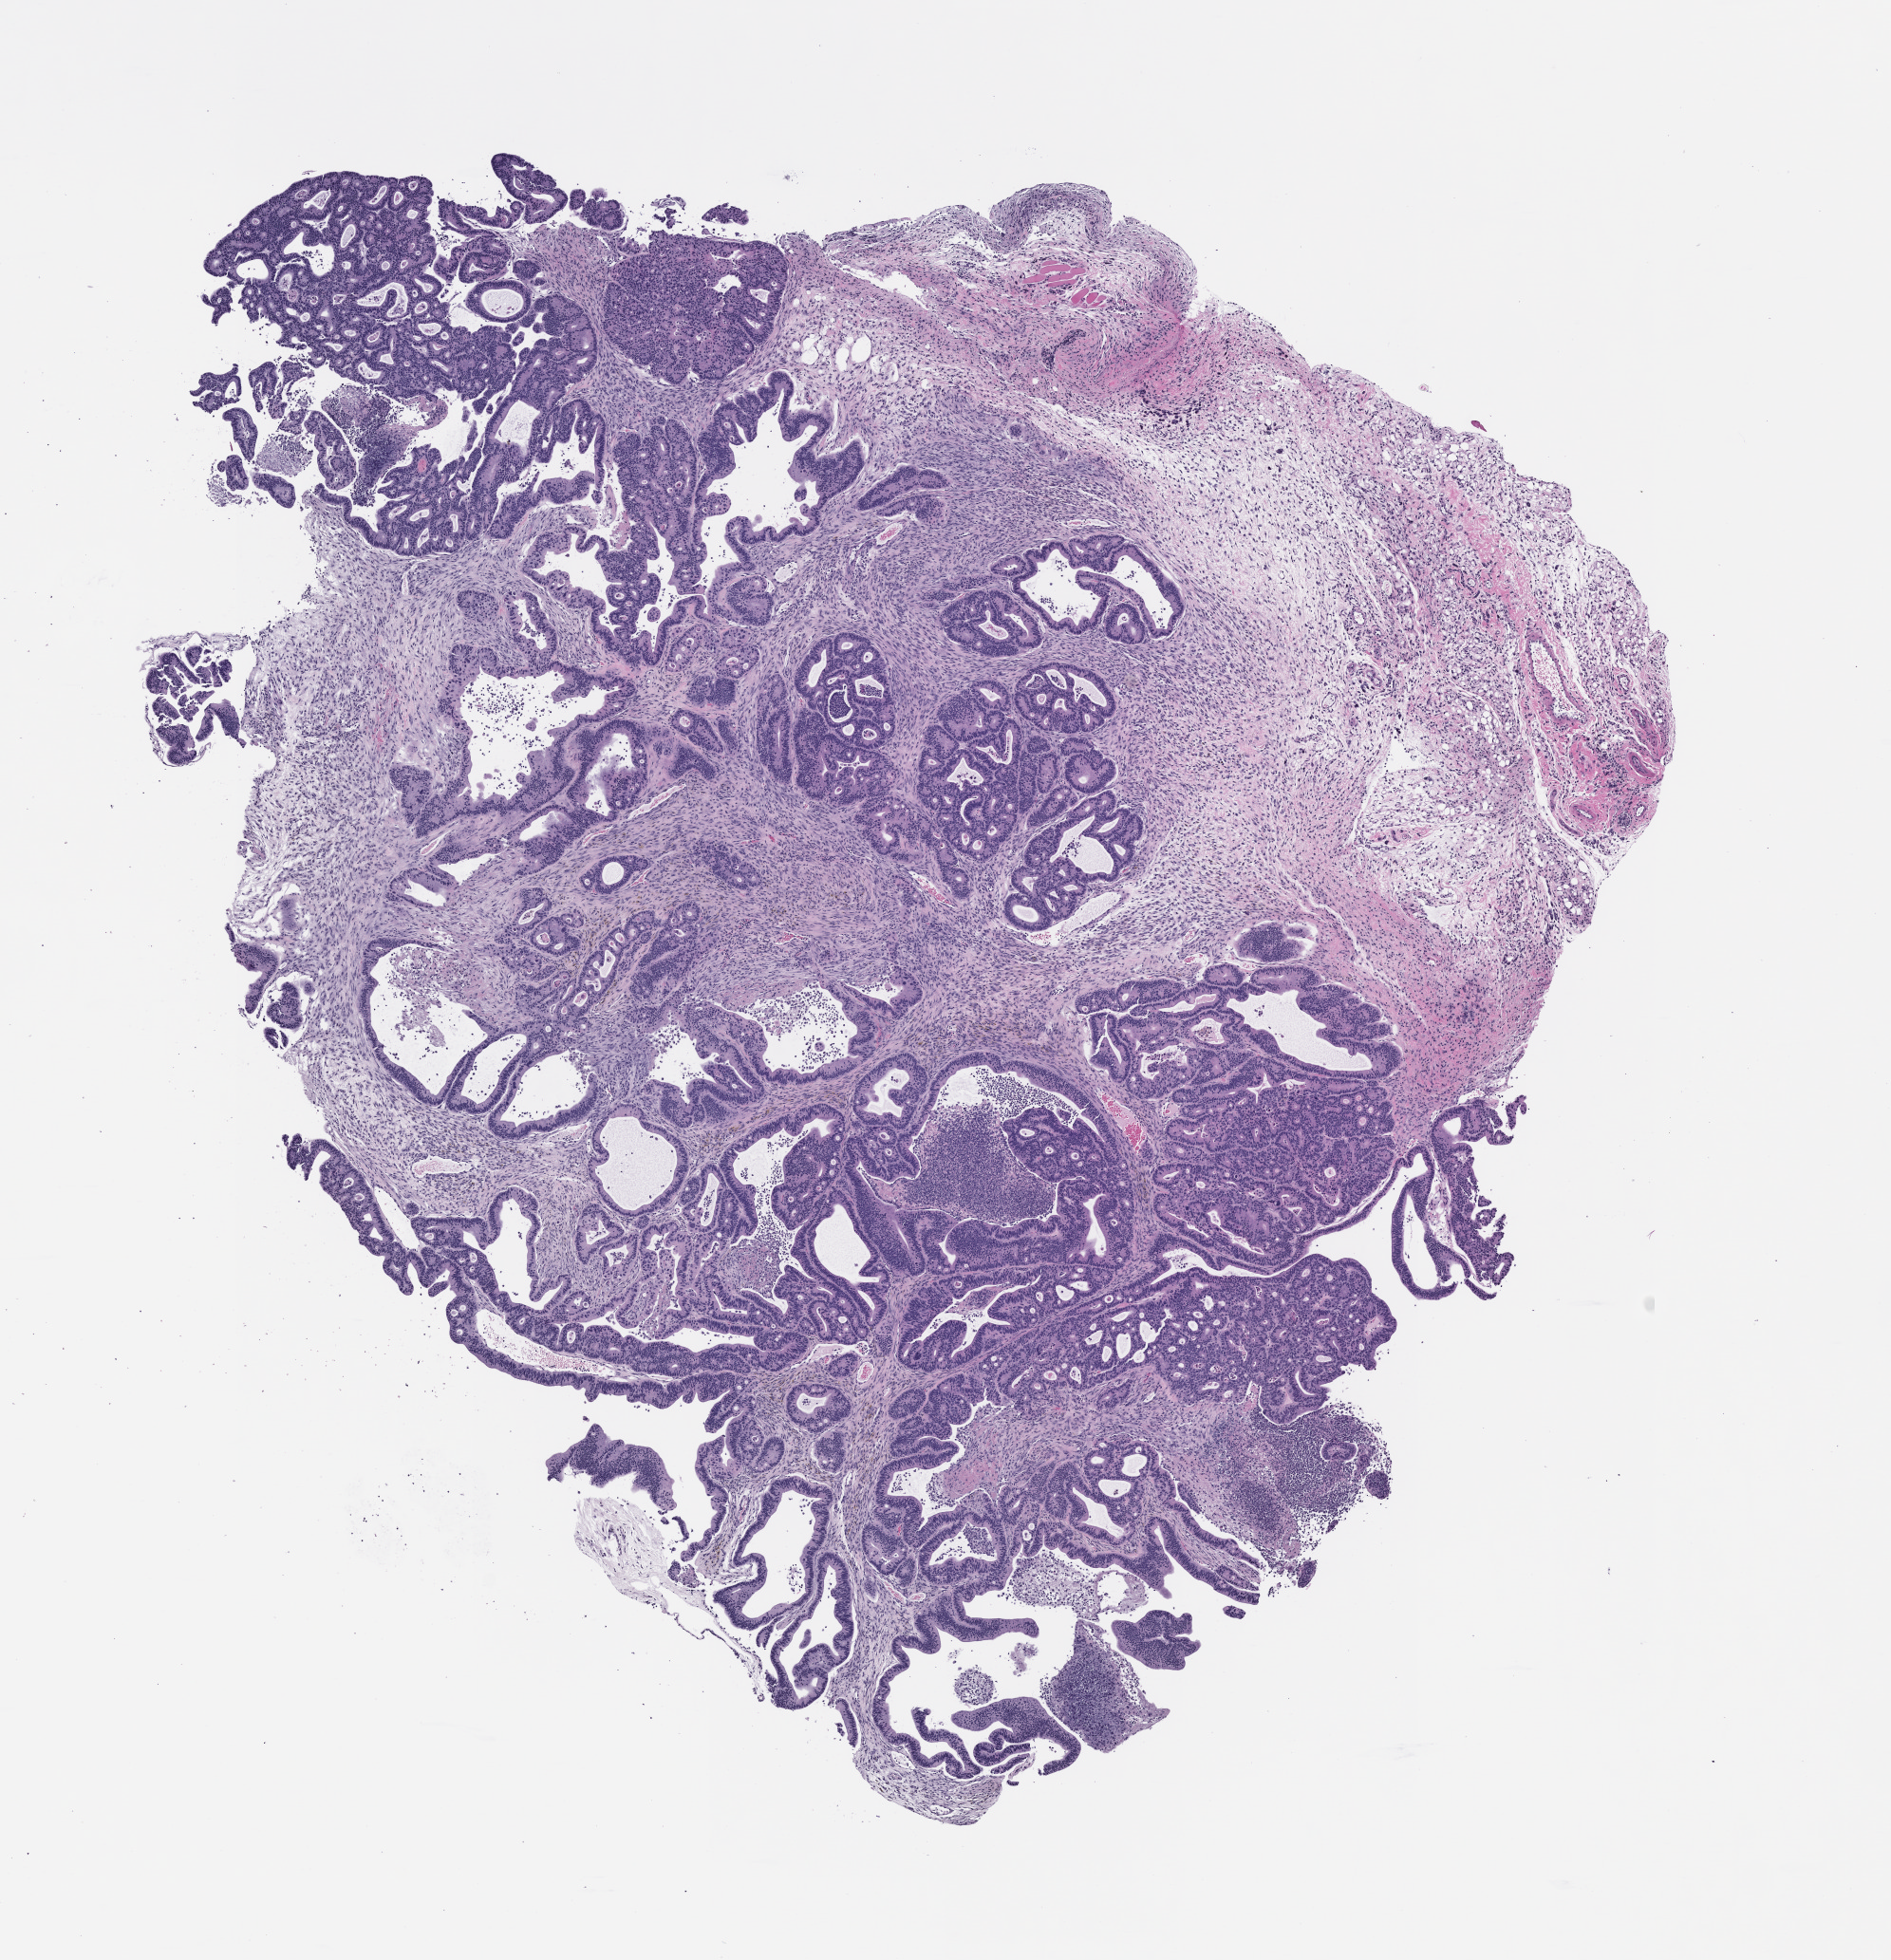
Haematoxylin and eosin whole-slide image of a patient-derived xenograft (PDX) tumor grown in a mouse, passage 2, shown as a low-resolution overview of the whole scanned area (about 8.0 x 8.3 mm); formalin-fixed paraffin-embedded section; originating tumor site category: colon.
Originating patient diagnosis: Colon Adenocarcinoma.